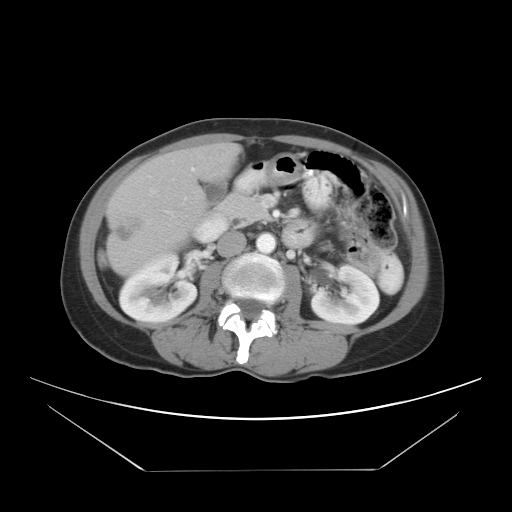
Contrast-enhanced abdominal CT, one axial slice; slice 11 of 30 in the series (ordered by position); reconstruction kernel STANDARD; intravenous contrast given; soft-tissue window (W 400 / L 40 HU); 7.5 mm slice thickness; 512 × 512 image matrix. Female patient, age 54 years. Case-level facts recorded for this patient, not image findings: diagnosis: colorectal cancer liver metastases, imaged before liver resection.
Outlined on this slice (outlined manually by an expert reader):
- liver: bounding box [x1, y1, x2, y2] px = [108, 145, 236, 272]
- planned liver remnant (the part of the liver to remain after resection): [122, 145, 236, 232]
- portal vein (with intrahepatic branches): [172, 166, 195, 181]
- liver metastasis: [116, 216, 146, 243]